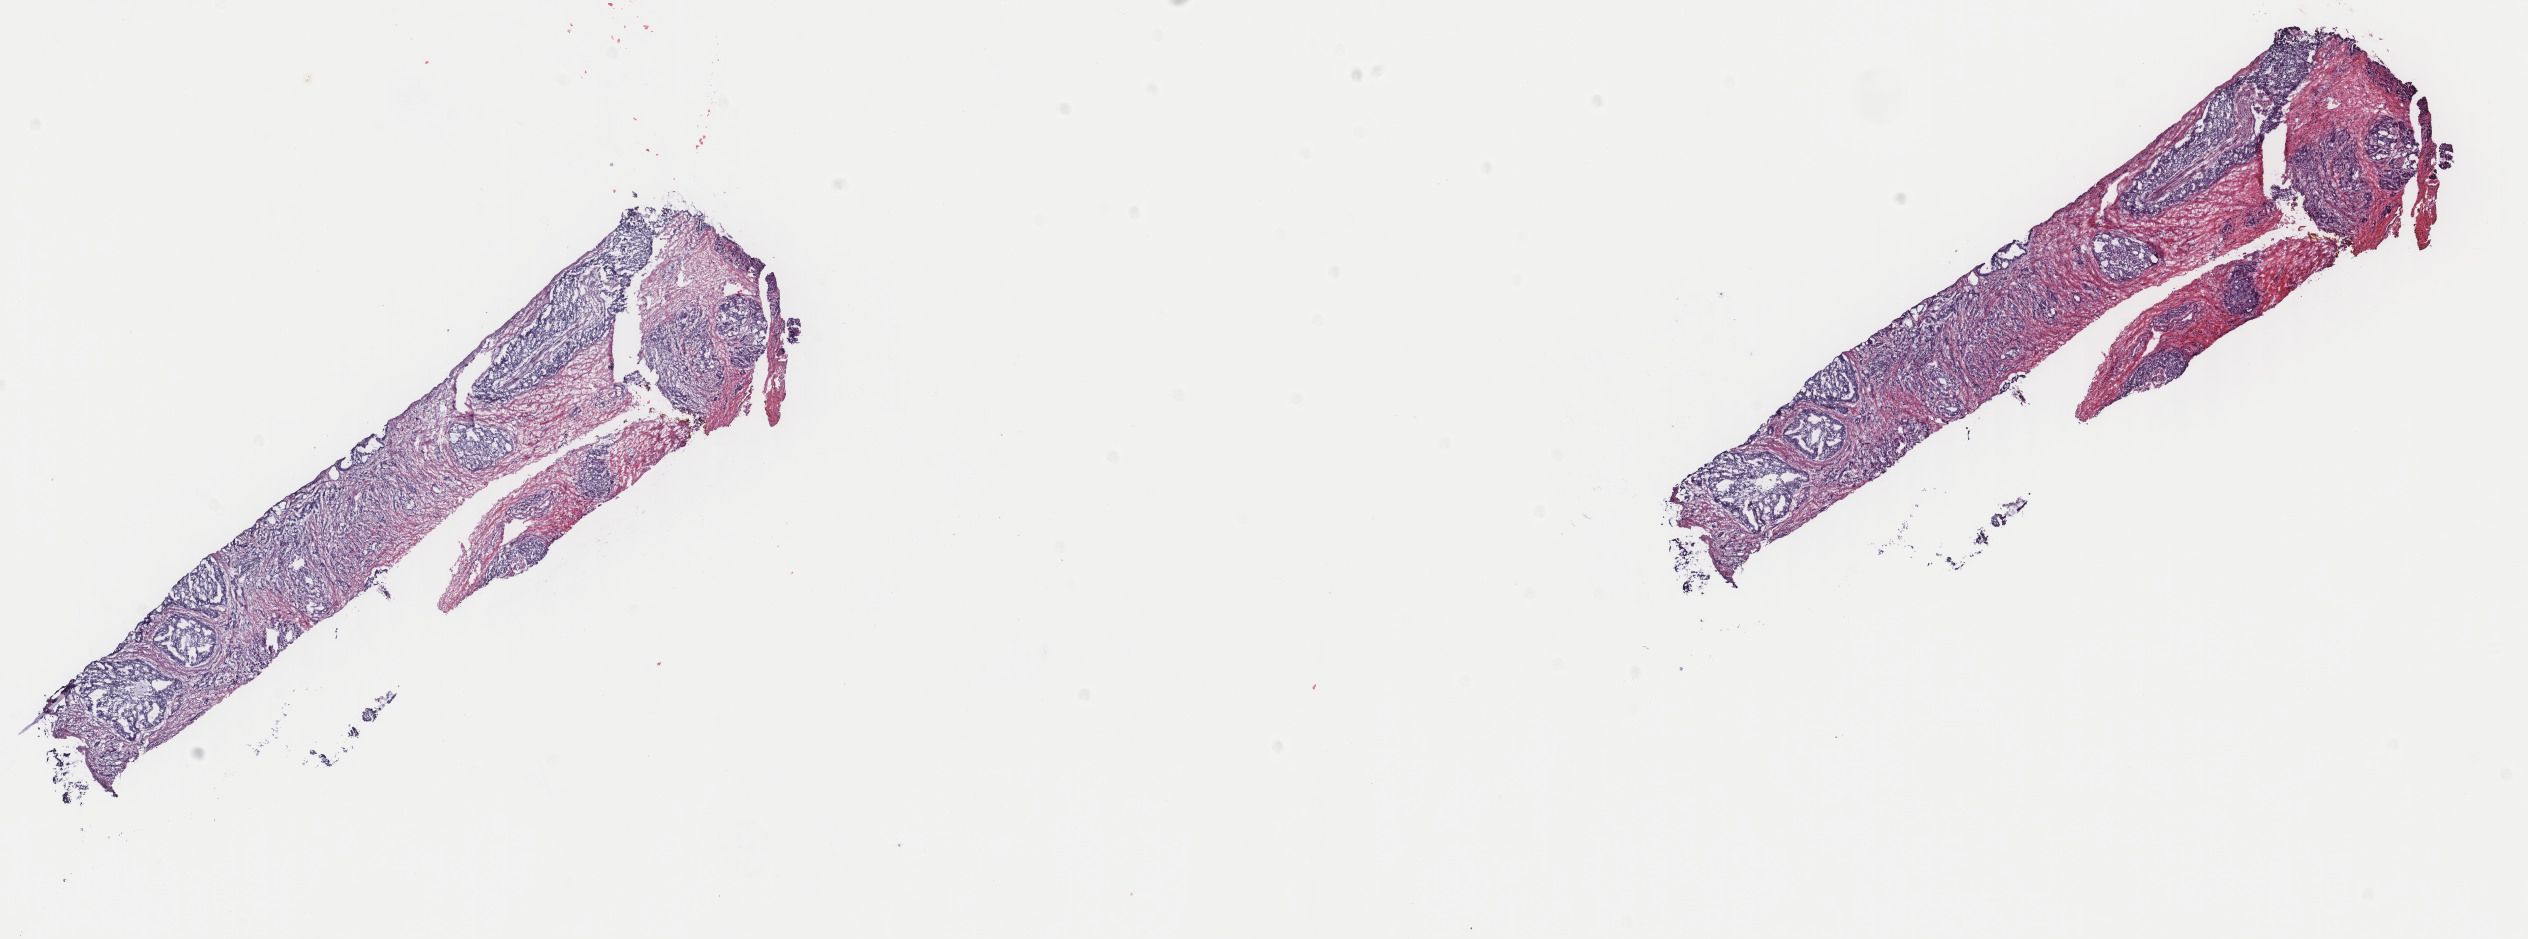
Hematoxylin and eosin (H&E) stained whole-slide image, whole scanned area (about 20.1 x 7.5 mm) shown as a low-resolution overview, frozen section from the top of the tissue portion, sample: primary tumour, prostate. Male patient; age at initial diagnosis 71 years. Gleason score: 8 (4+4). Pathologist review of this section (percent, as recorded): tumour cells 65%, tumour nuclei 100%, normal cells 0%, stromal cells 35%, necrosis 0%. Infiltration values recorded for this section: lymphocyte infiltration 1%, monocyte infiltration 0%, neutrophil infiltration 0%.
Pathologic diagnosis: Infiltrating duct carcinoma, NOS (prostate gland). Laterality: bilateral. Lymph nodes positive (case pathology): 0 of 17 examined.